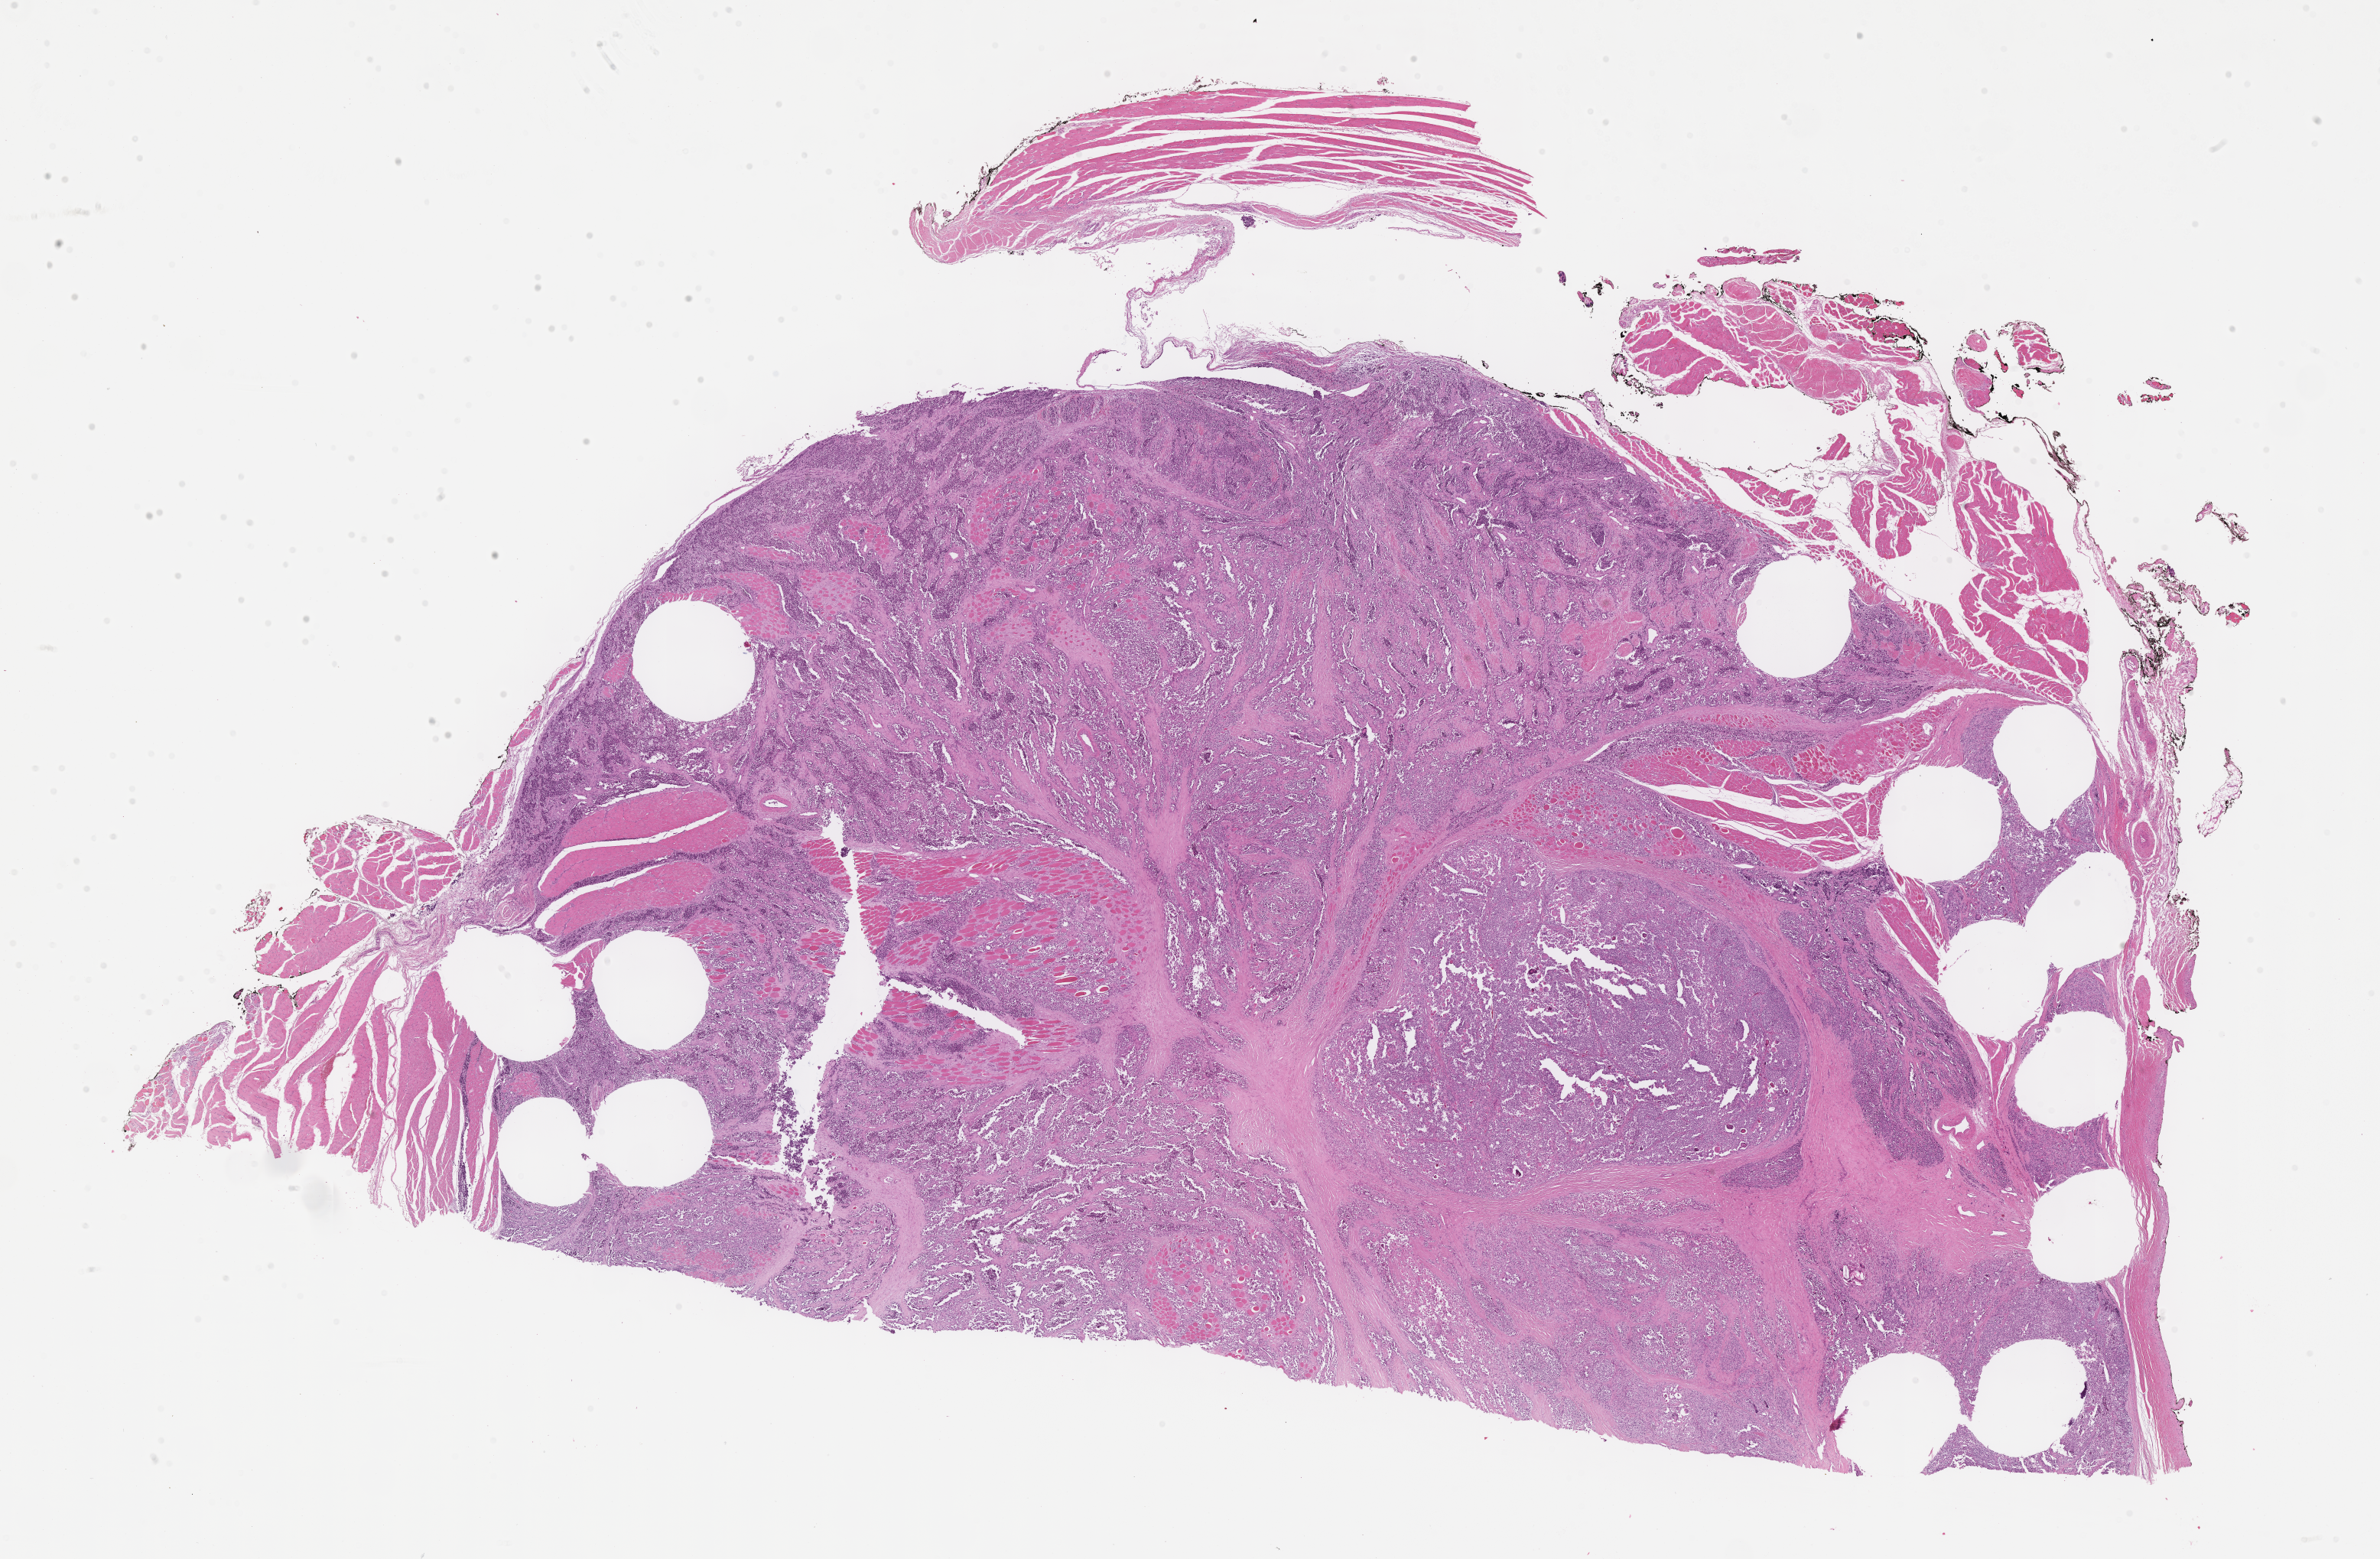
Digitized hematoxylin and eosin (H&E)-stained section of tumor tissue, whole scanned area (about 25.2 x 16.5 mm) shown as a low-resolution overview; formalin-fixed paraffin-embedded section; site: hand, left. Male patient, age at diagnosis 12.0 years.
* metastatic status at presentation (as recorded): non-metastatic
* stage (as recorded): 2
* diagnosis: rhabdomyosarcoma; histological classification: alveolar rhabdomyosarcoma